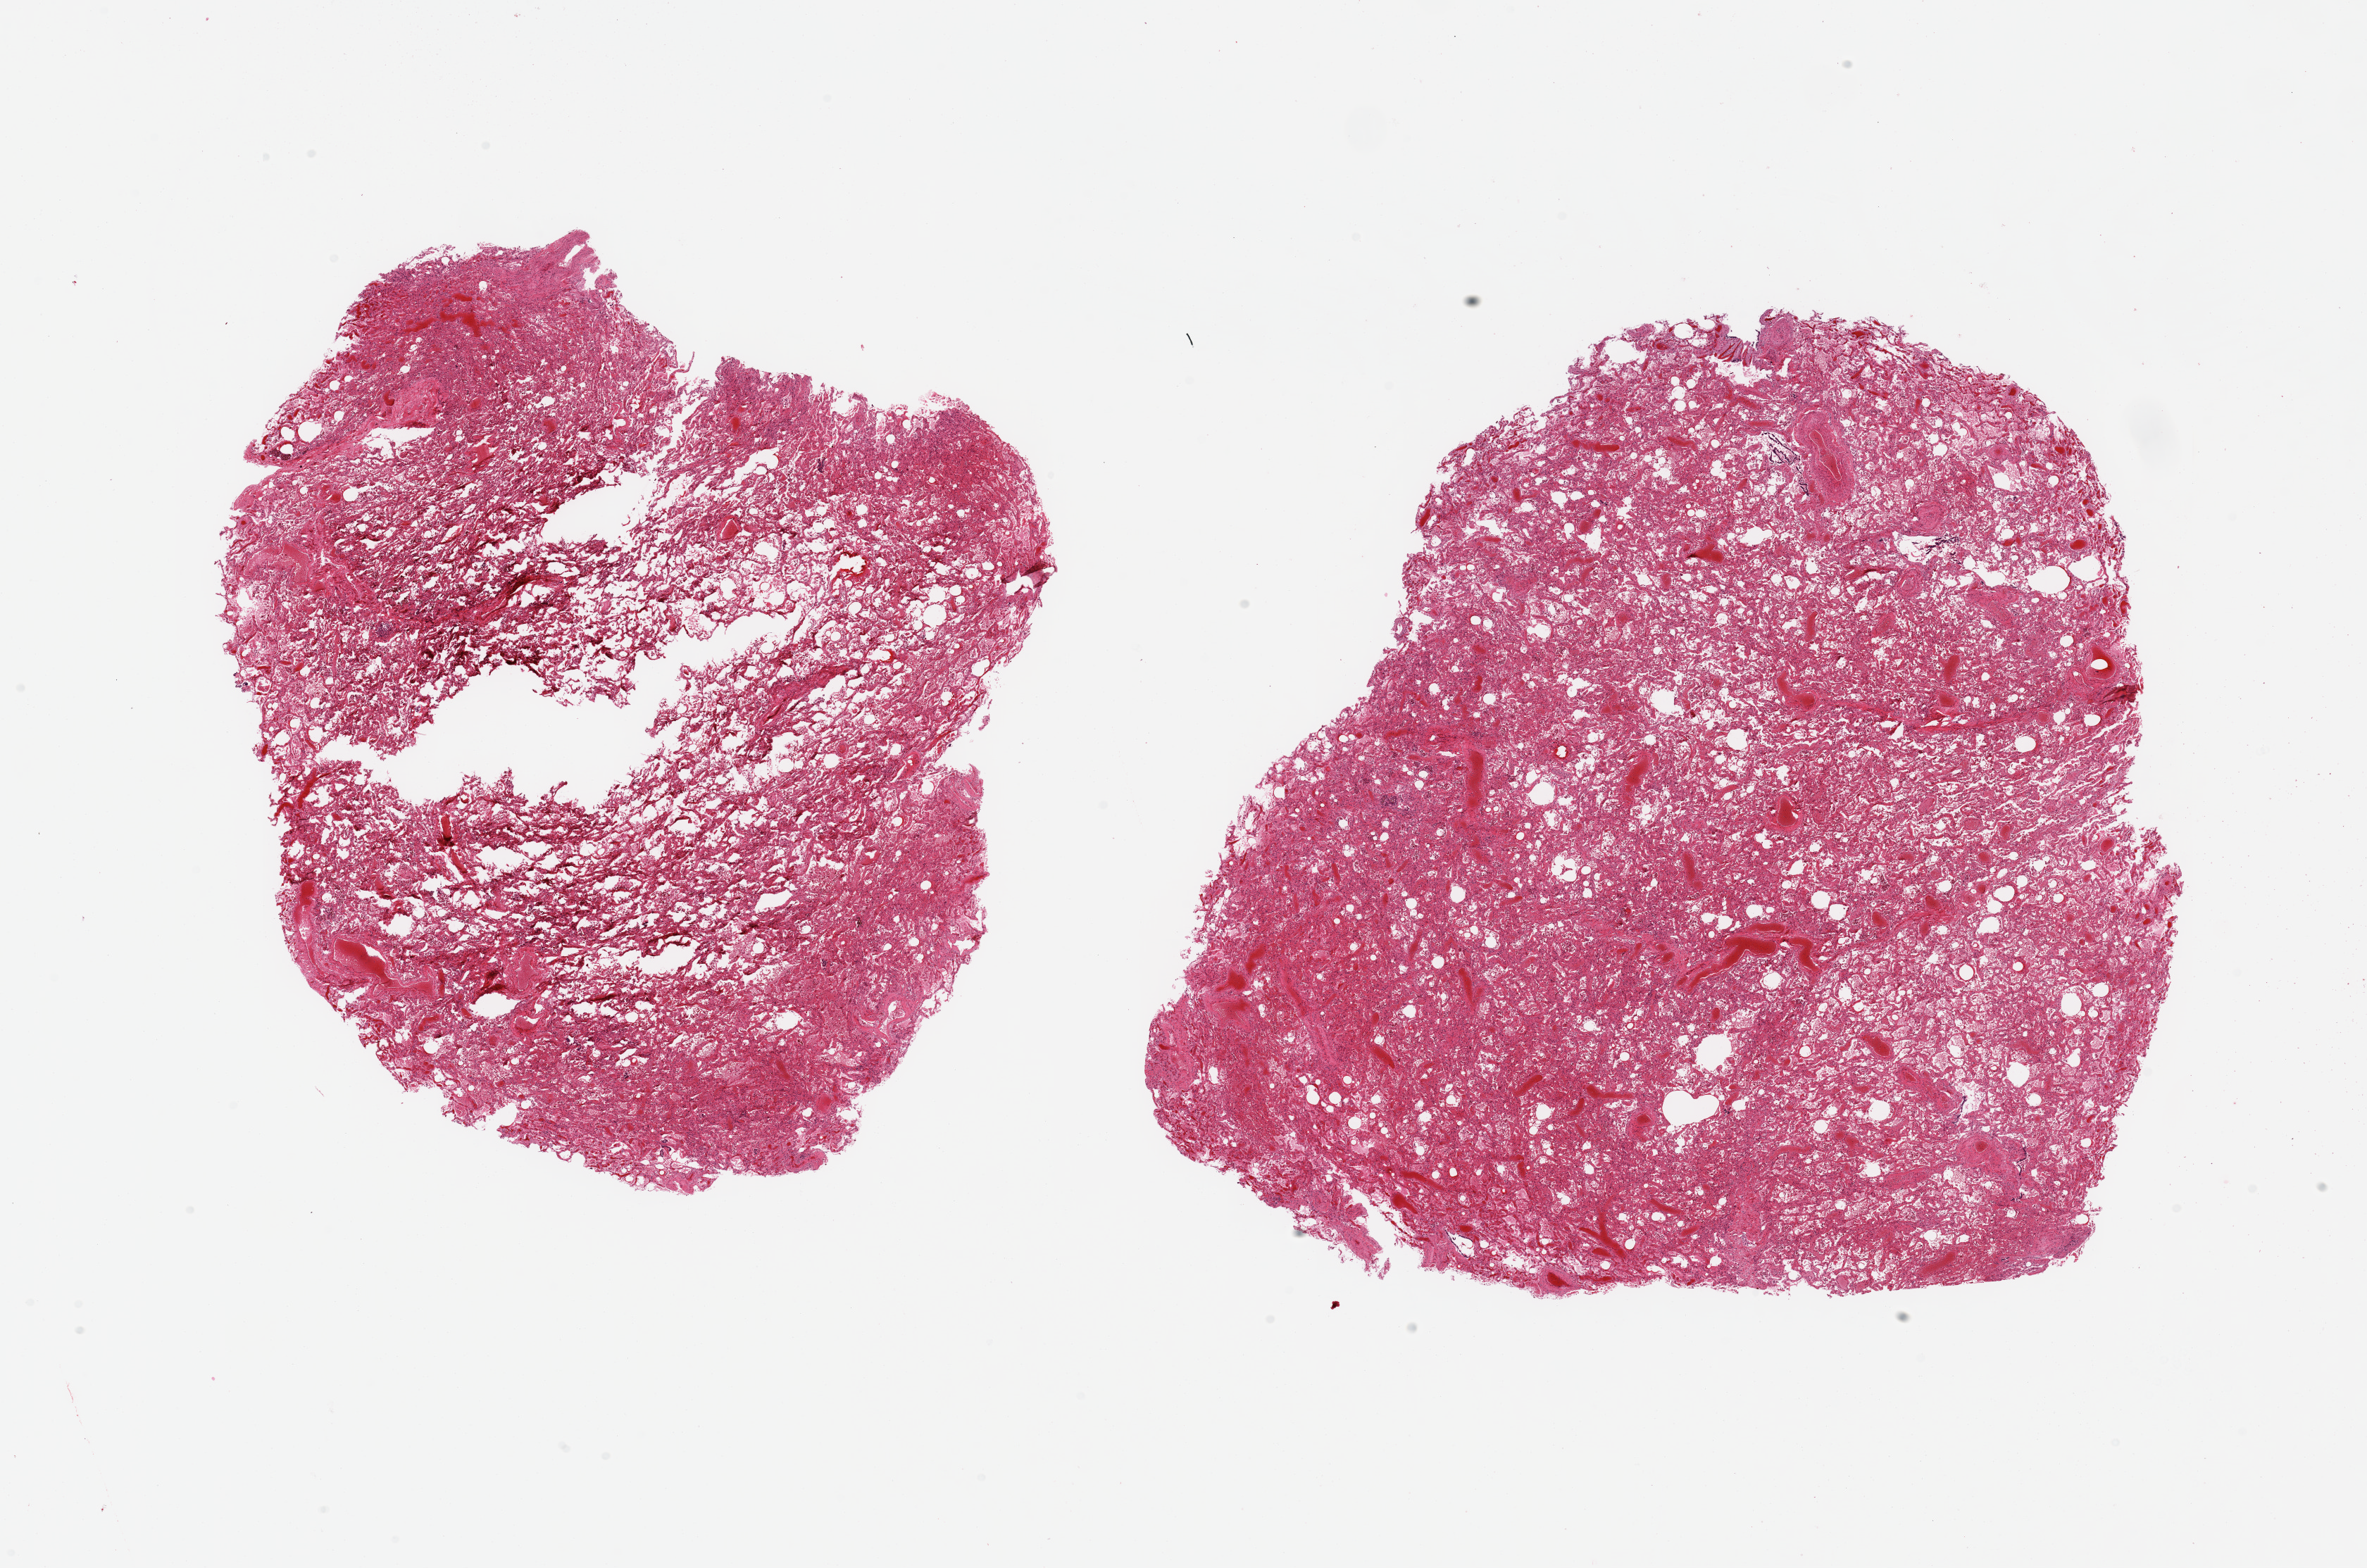
Digitized hematoxylin and eosin (H&E)-stained section — whole scanned area (about 26.6 x 17.6 mm) shown as a low-resolution overview; PAXgene-fixed paraffin-embedded (PFPE) section; target tissue: lung; tissue donor sample. Donor: male.
* review note (as recorded): 2 pieces; moderately congested; scattered alveolar hemorrhages